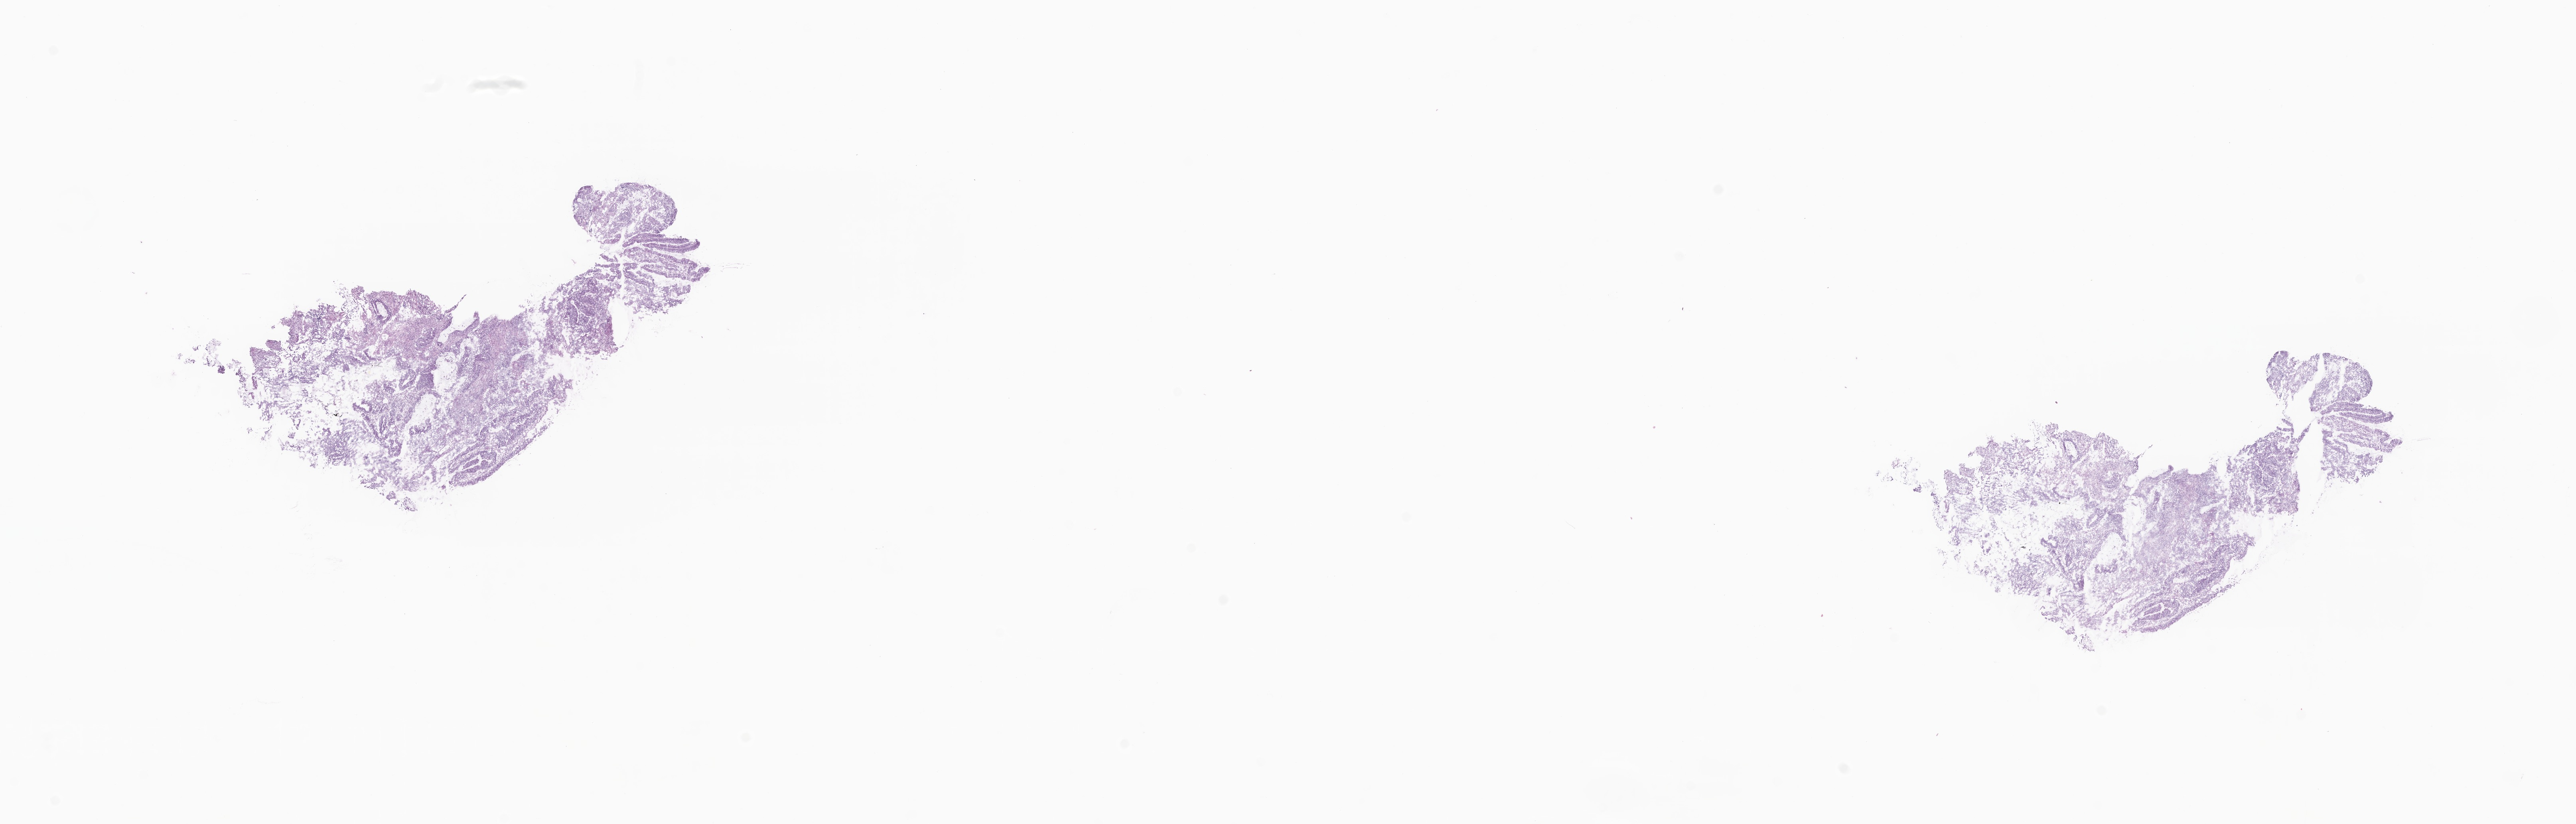
Digitized hematoxylin and eosin (H&E)-stained section, whole scanned area (about 27.2 x 8.7 mm) shown as a low-resolution overview. Frozen section (tissue freezing medium). Specimen: primary tumor. Anatomic site: transverse colon. Patient: female. Pathologist review of this section (percent, as recorded): tumor cells 100%, tumor nuclei 70%, stromal cells 0%, necrosis 0%, normal cells 0%. Inflammatory infiltration, as recorded: lymphocyte infiltration 0%, monocyte infiltration 0%, neutrophil infiltration 0%.
• histologic diagnosis: Adenocarcinoma, NOS
• section: top of the tissue portion